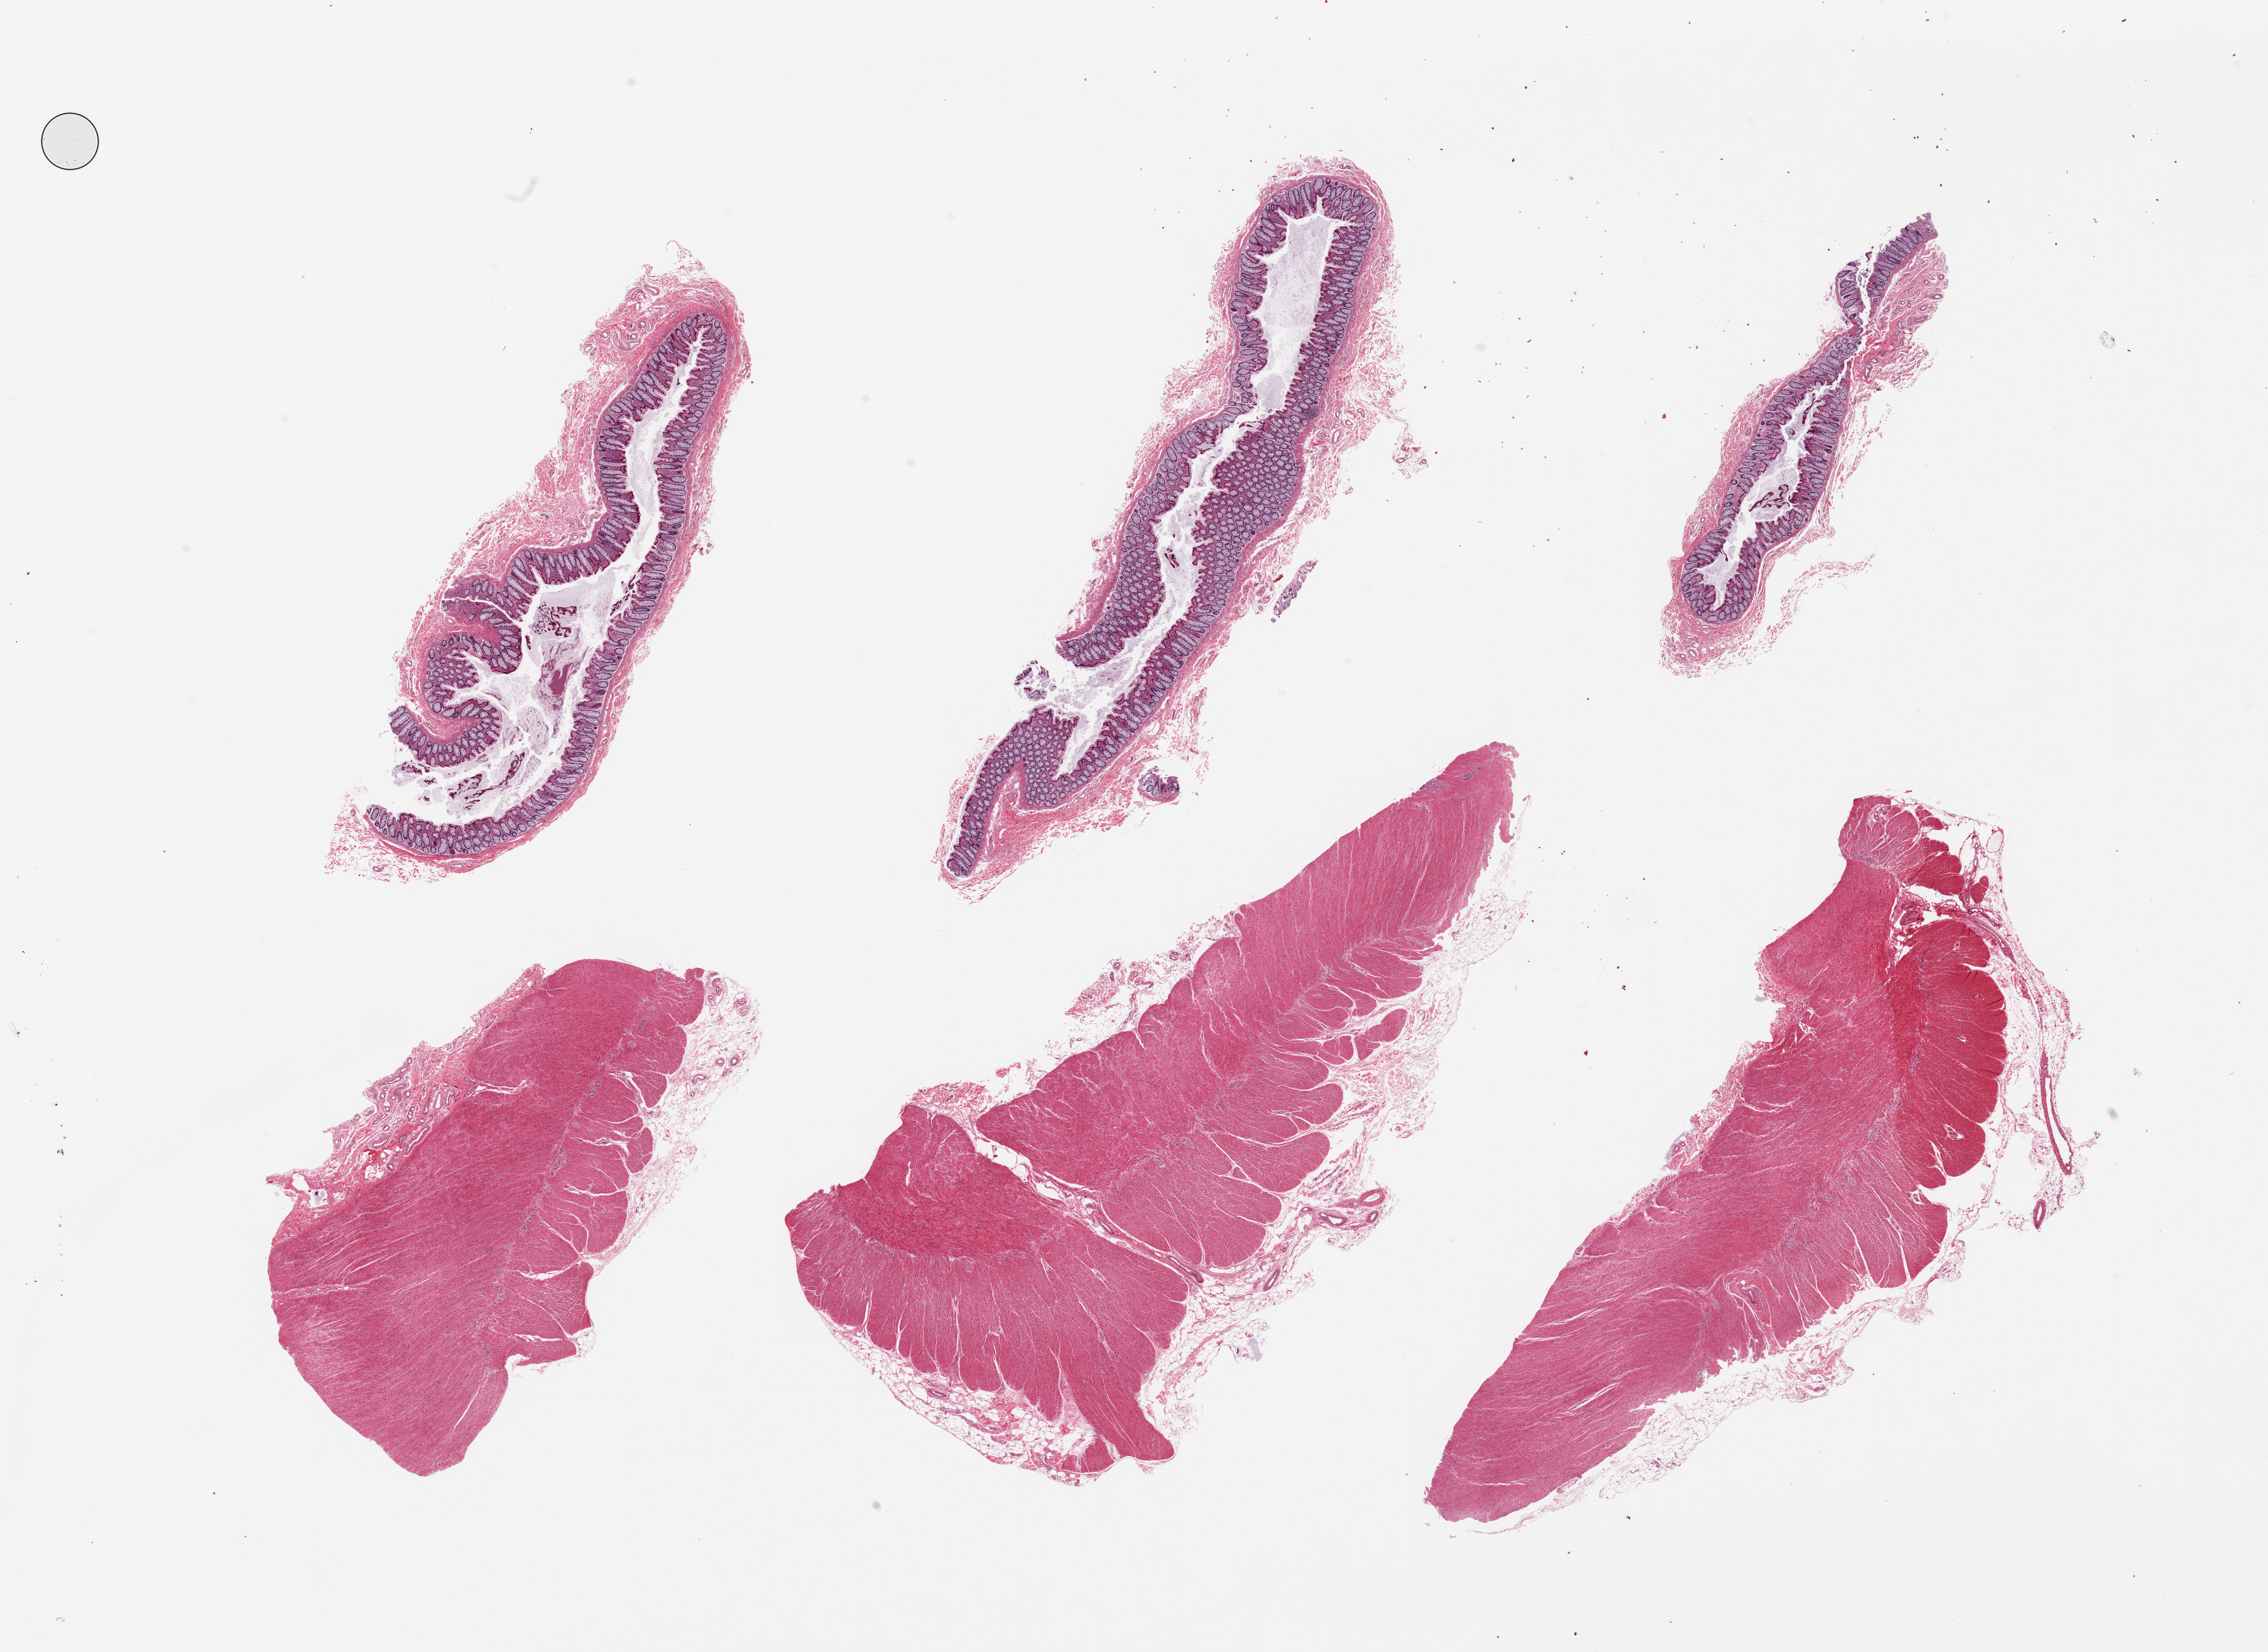
Digitized H&E-stained section, shown as a low-resolution overview of the whole scanned area (about 28.5 x 20.8 mm, from a 20x scan); PAXgene-fixed, paraffin-embedded tissue; sampled site (target tissue): sigmoid colon; donor tissue sample. Donor sex: female.
Pathologist's review note for this sample: 6 pieces; 3 are muscularis propria [target]; 3 are mucosa [not target].